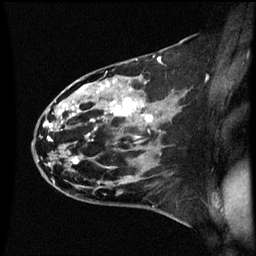
Breast MRI (dynamic contrast-enhanced), one sagittal slice; position 36 of 60 along the scan axis; dynamic contrast-enhanced series, image 2 of 3 at this slice position (ordered by acquisition); 1.5 T; TE 4.2 ms, TR 8.9 ms; 256 × 256 image matrix, field of view 200 × 200 mm. Female patient, age 44 years. Case-level facts recorded for this patient, not image findings: setting: breast cancer imaged before/during neoadjuvant chemotherapy; receptor status: HR-positive, HER2-negative.
Outlined on this slice (semi-automatically segmented with operator editing):
- analysis volume of interest (the breast-tissue region the enhancement analysis was run in; not a lesion): bounding box (x1, y1, x2, y2) in pixels: (43, 78, 153, 189)
- tumour enhancement mask (voxels above the 70 % enhancement threshold inside the analysis volume of interest): (45, 84, 153, 163)